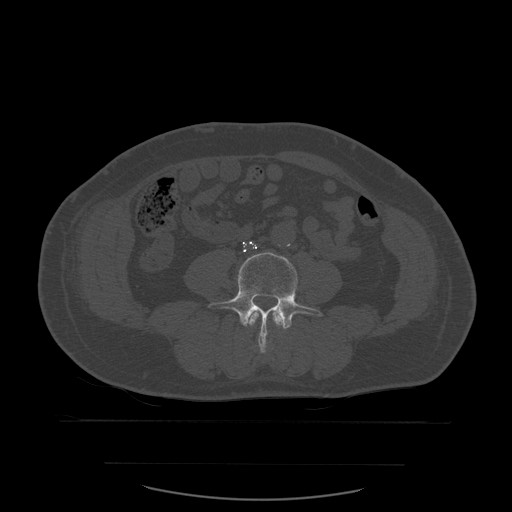
CT including the spine, one axial slice. Position 171 of 590 along the scan axis. Bone window (W 1800 / L 400 HU). 1.25 mm slice thickness. 512 × 512 image matrix, field of view 479 × 479 mm. Patient age 71 years. From the clinical record (not read from this slice): primary cancer: lung; vertebrae with lytic lesions (as recorded): T1, T2, L5, S1.
Structures marked on this image (semi-automatically segmented with operator editing):
- L3 vertebra: bounding box <248,312,284,353> (left, top, right, bottom; pixels)
- L4 vertebra: <209,252,321,352>